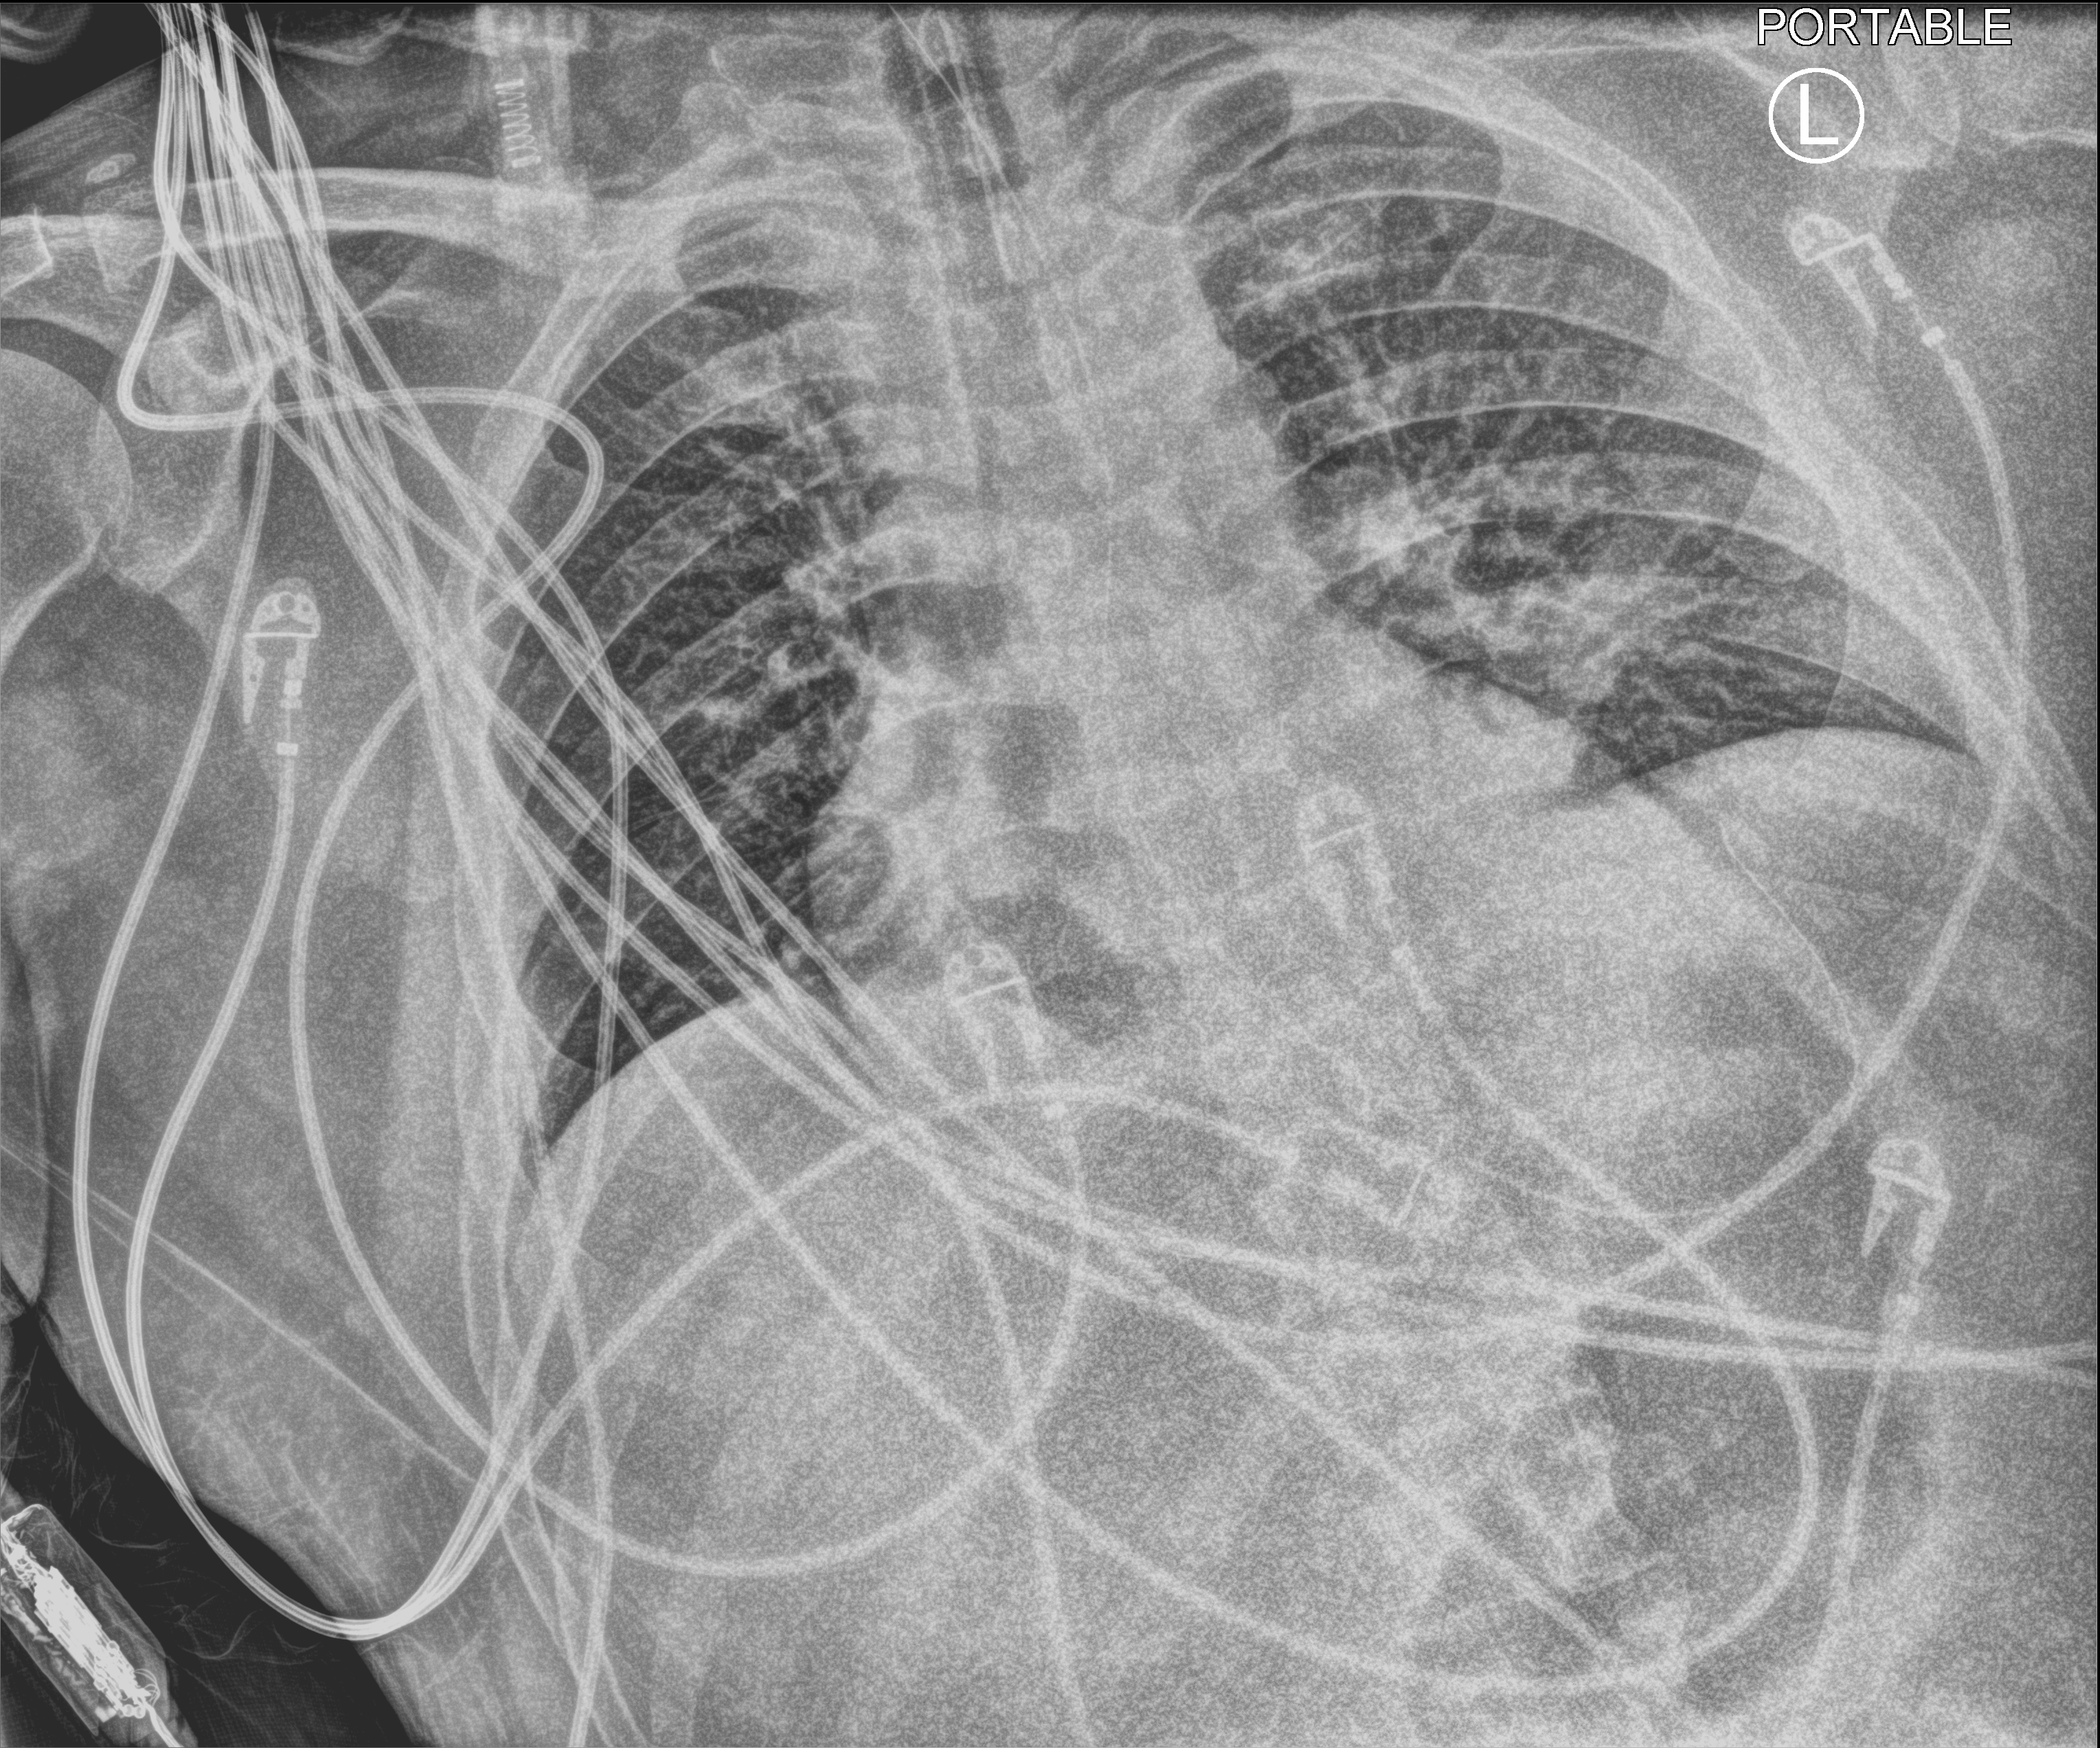
Chest X-ray (portable), anteroposterior (AP) projection. Male patient hospitalised with COVID-19, age 18–59 years.
From the hospital-stay record, not from the radiograph (when in the stay this image was taken is not recorded): admitted to intensive care during this hospital stay: yes.